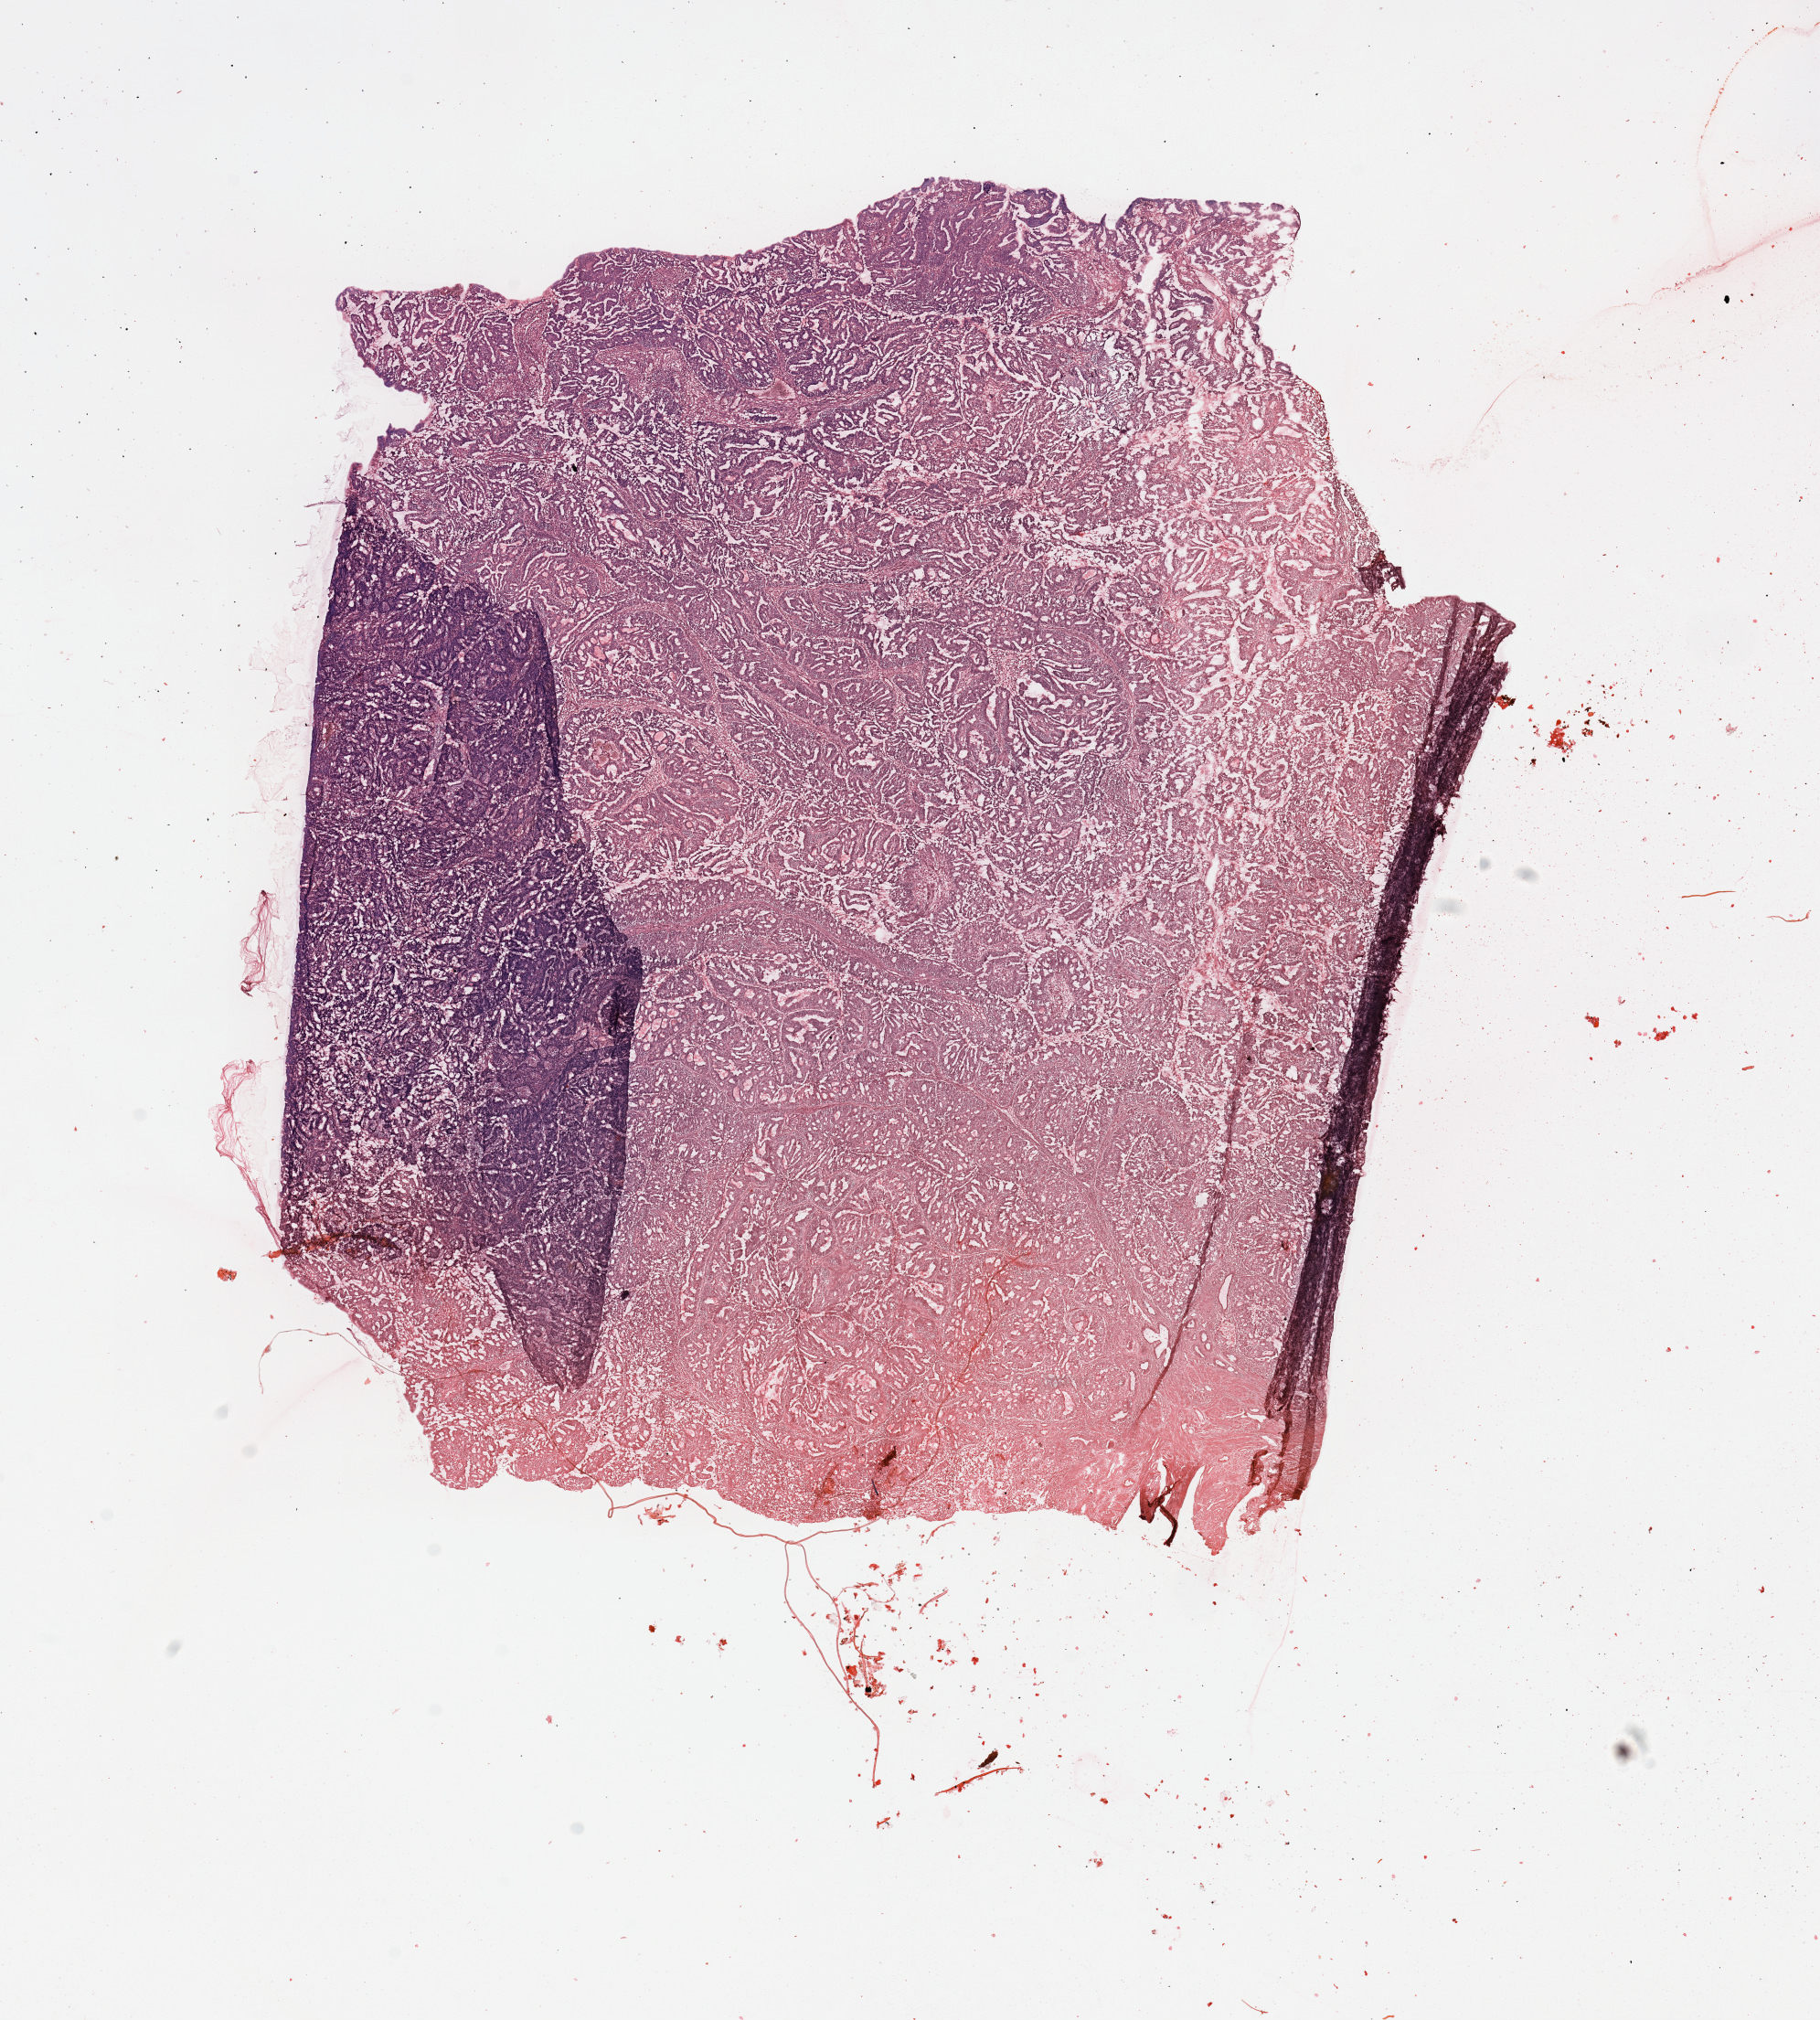
Whole-slide histology image, H&E-stained, low-resolution overview of the scanned area, about 15.8 x 17.5 mm. Uterus, tumour tissue. Female, 59 y/o. Histologic grade: G2 (moderately differentiated).
* AJCC pathologic stage: I
* diagnosis: Endometrioid adenocarcinoma, NOS